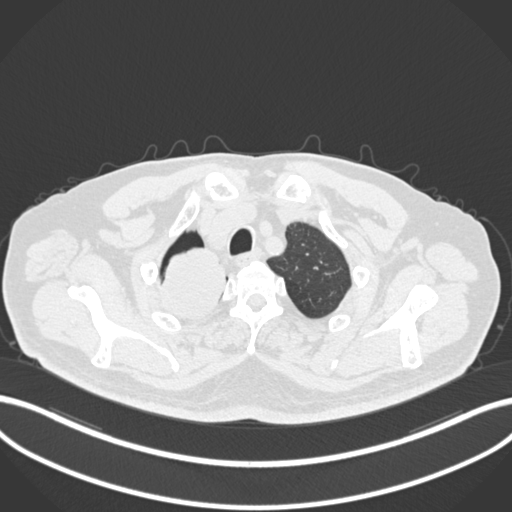
Chest CT, one axial slice; position 188 of 218 along the scan axis; reconstruction kernel B30f; 120 kVp; lung window (W 1500 / L -600 HU); 512 × 512 image matrix, field of view 400 × 400 mm. Male patient, age 68 years. From the clinical record (not read from this slice): clinical TNM (as recorded): T2a N0 M0.
Annotated regions visible in this slice (rectangle marked by the reading radiologist):
- lung tumour (recorded histology: adenocarcinoma): bounding box <154,245,228,323> (left, top, right, bottom; pixels)